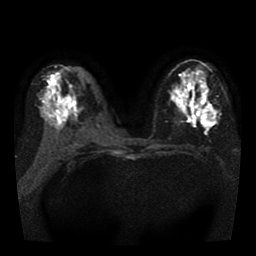
Breast MRI, one axial slice. Slice 18 of 41 in the series (ordered by position). Diffusion-weighted series; image 2 of 4 stored at this slice position (different b-values; order by instance number). 1.5 T. 256 × 256 image matrix. Female patient.
Annotated regions visible in this slice (manually delineated by an expert):
- tumour on diffusion-weighted imaging: box from (x=204, y=107) to (x=216, y=122) px